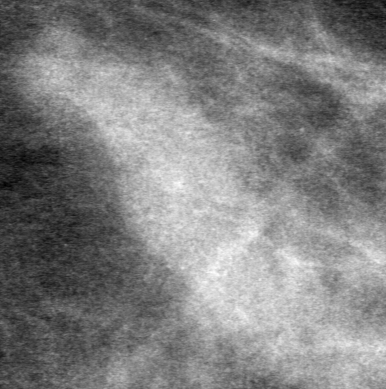
Region of interest cut from a scanned film mammogram (one marked finding); left breast; MLO view; BI-RADS breast density category 1 (scale 1–4).
Finding: mass, shape lobulated, margins obscured; BI-RADS assessment category 0 (incomplete: needs additional imaging); subtlety rating 2 on a 1 (subtle) to 5 (obvious) scale; pathology result (as recorded, not read from the image): benign.